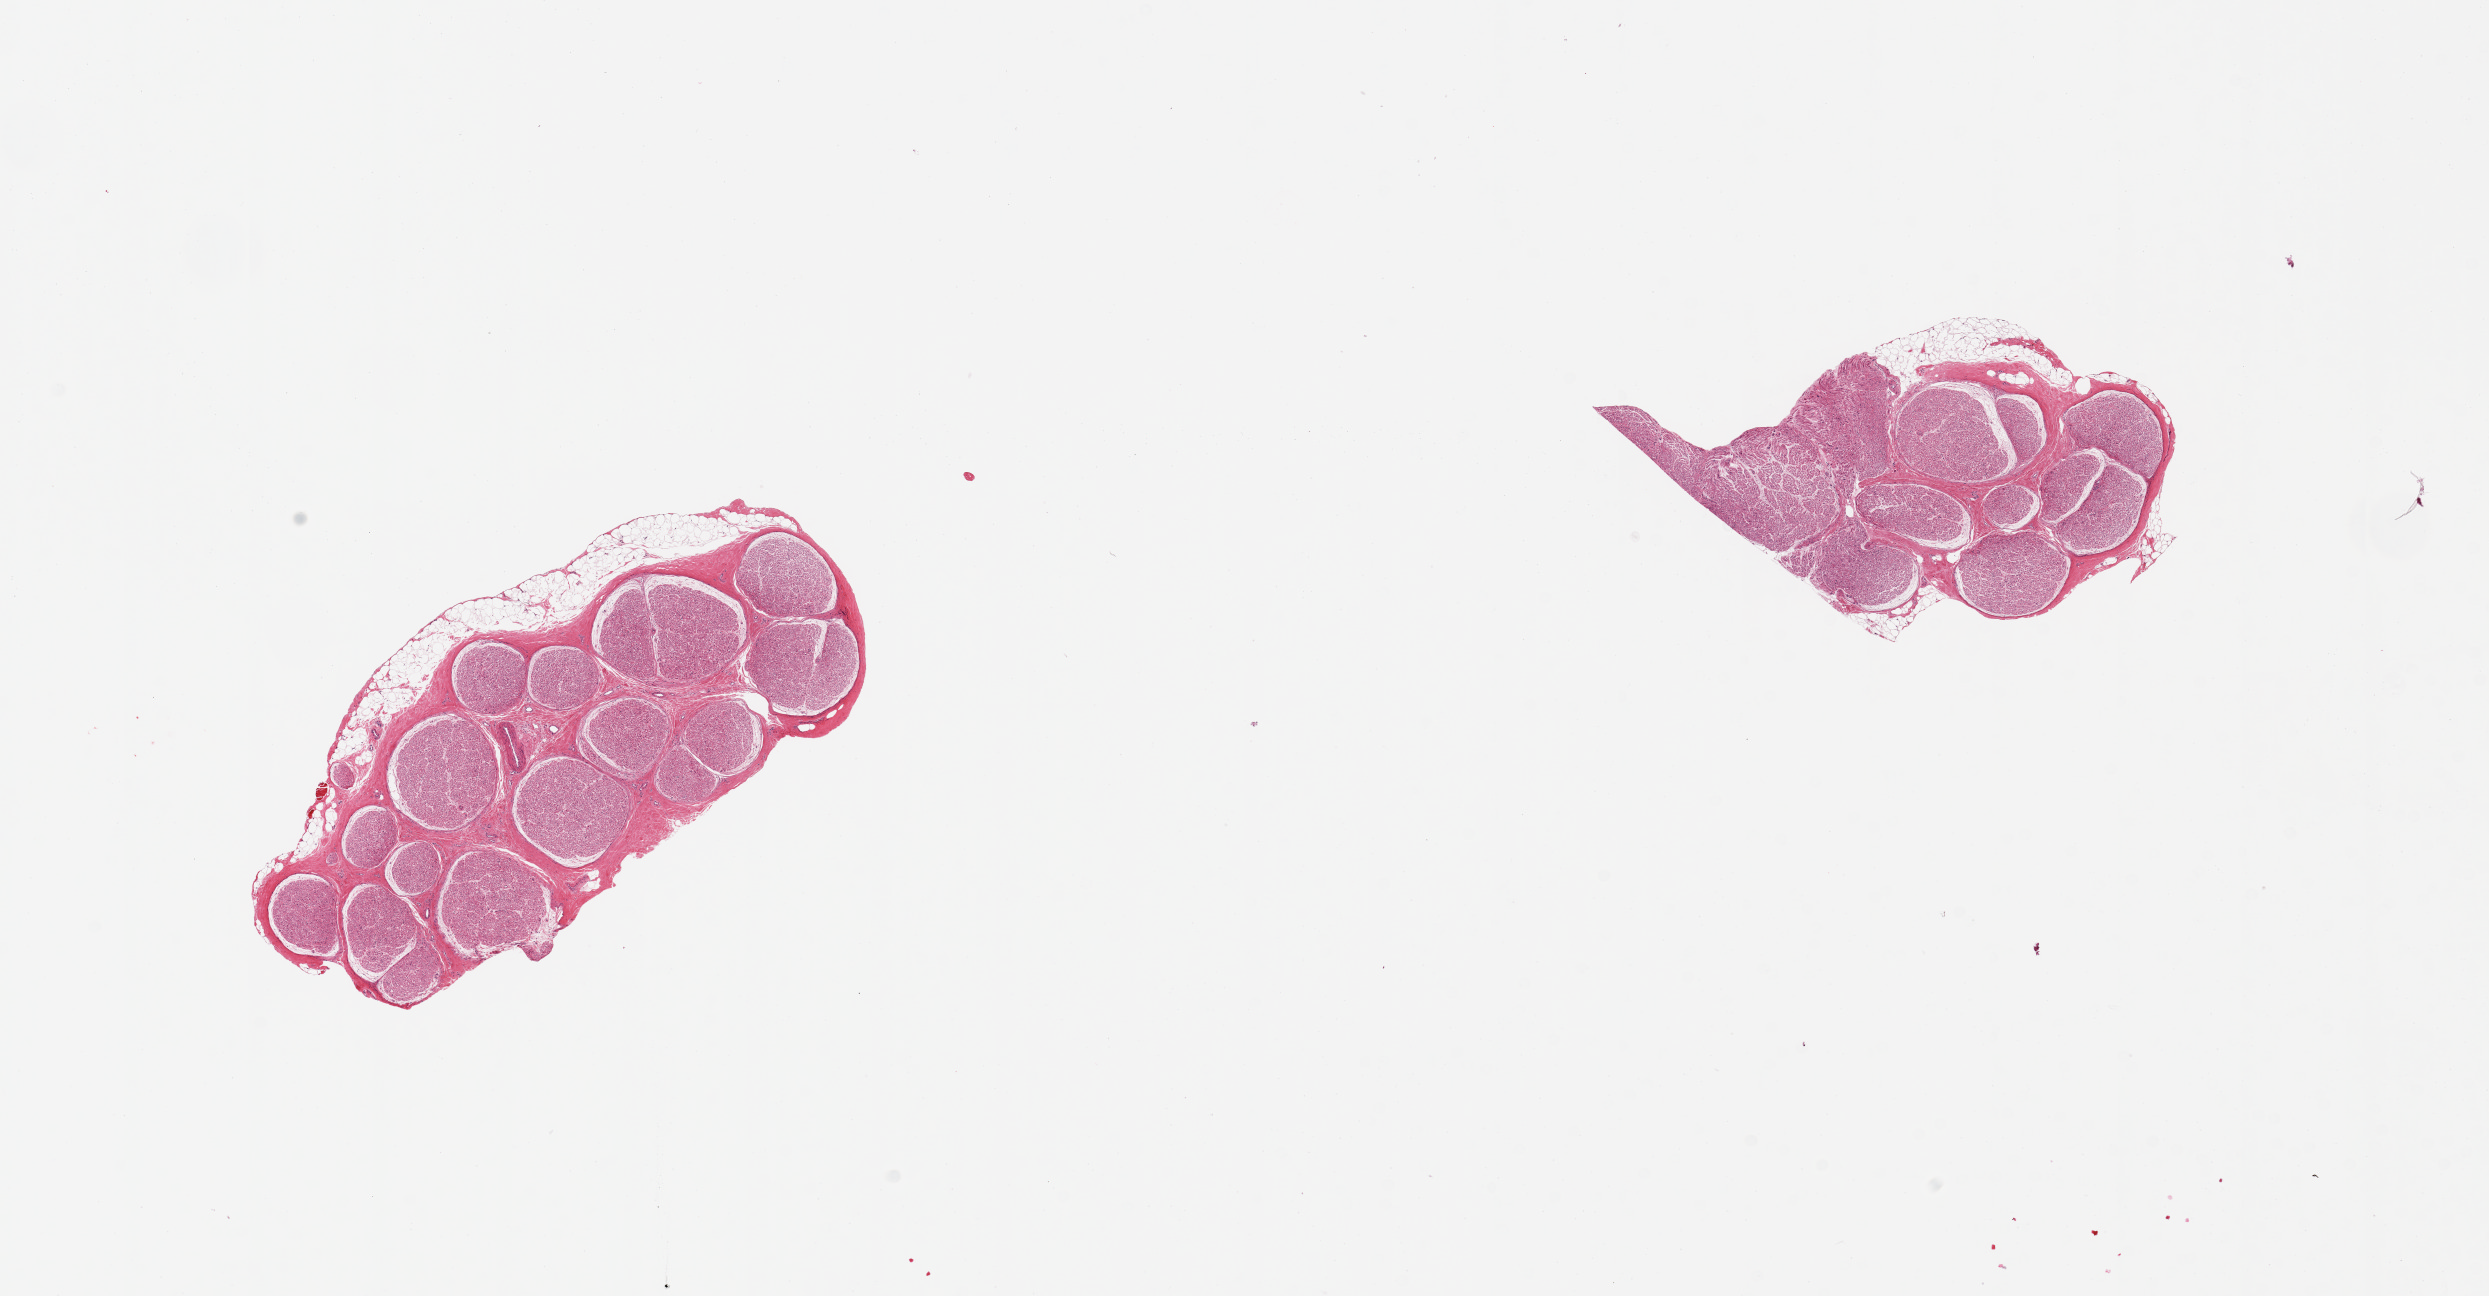
Hematoxylin and eosin (H&E) whole-slide image — whole scanned area (about 19.7 x 10.3 mm) shown as a low-resolution overview; PAXgene-fixed paraffin-embedded (PFPE) section; target tissue: tibial nerve; tissue donor sample.
Review note (as recorded): 2 pieces, trace adherent fat ~0.3mm.